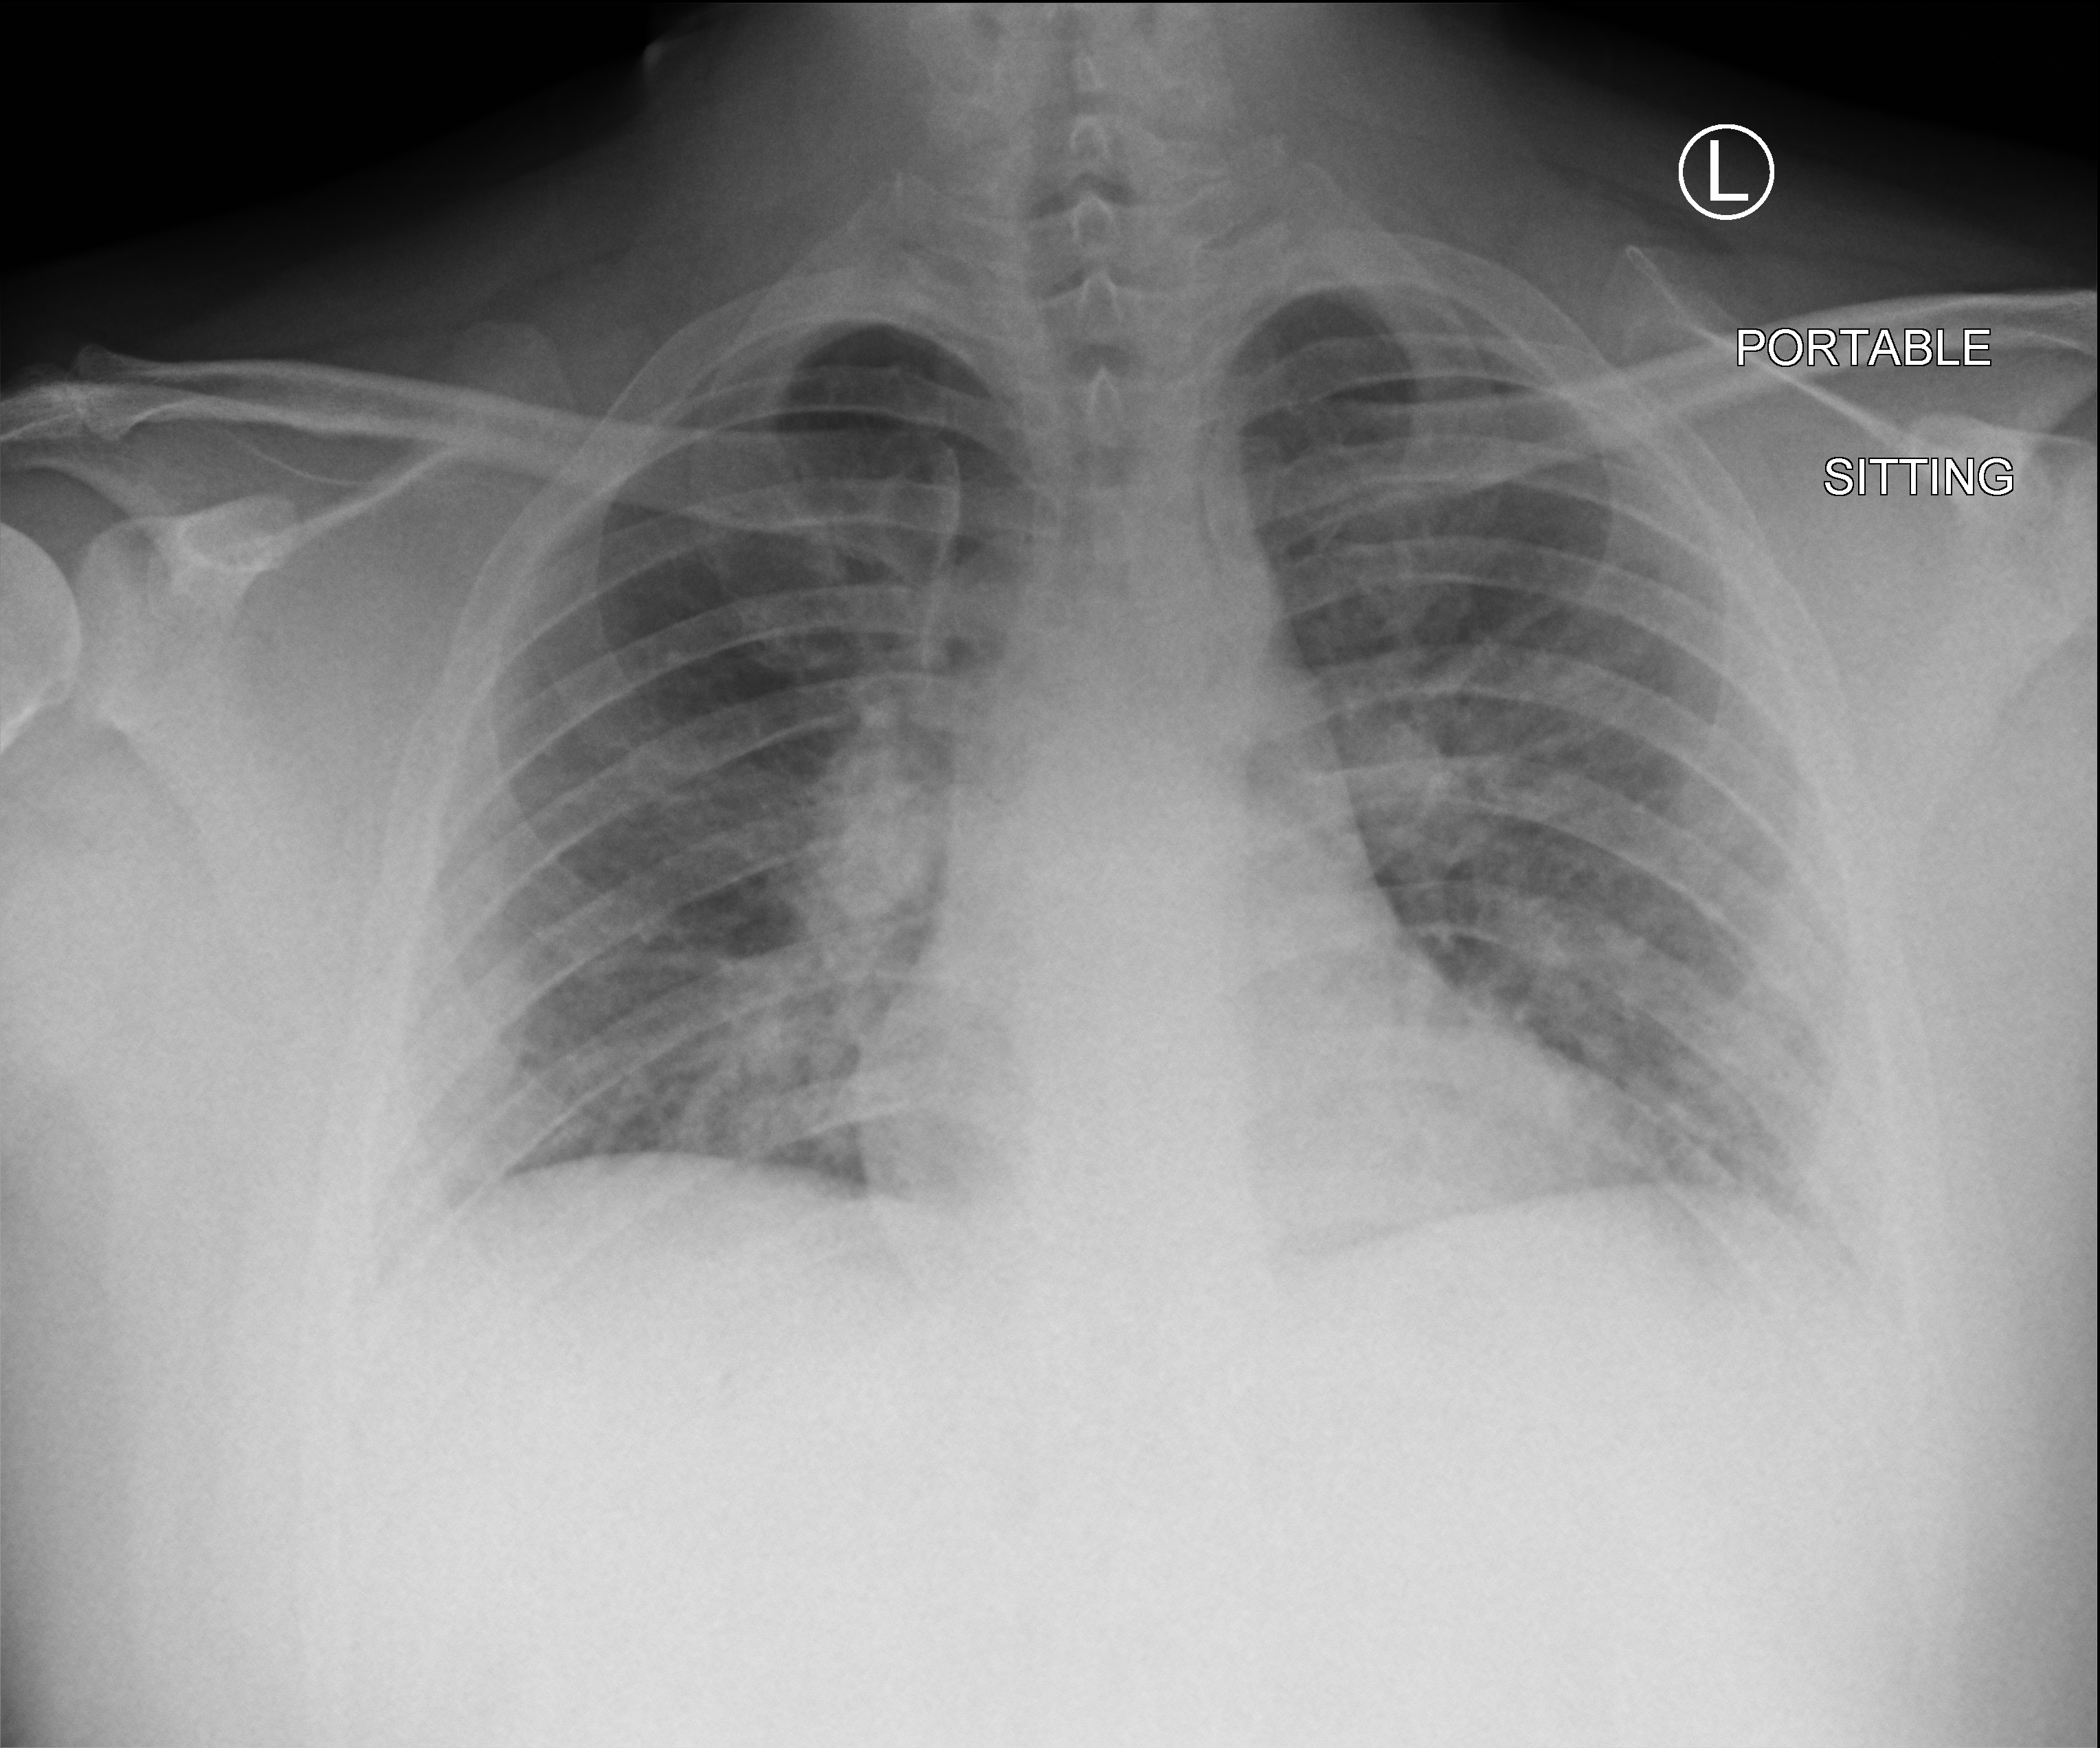
Chest X-ray (portable), anteroposterior (AP) projection. Male patient hospitalised with COVID-19, age 18–59 years.
From the hospital-stay record, not from the radiograph (when in the stay this image was taken is not recorded): mechanically ventilated during this hospital stay: no; COPD (admission record): no.